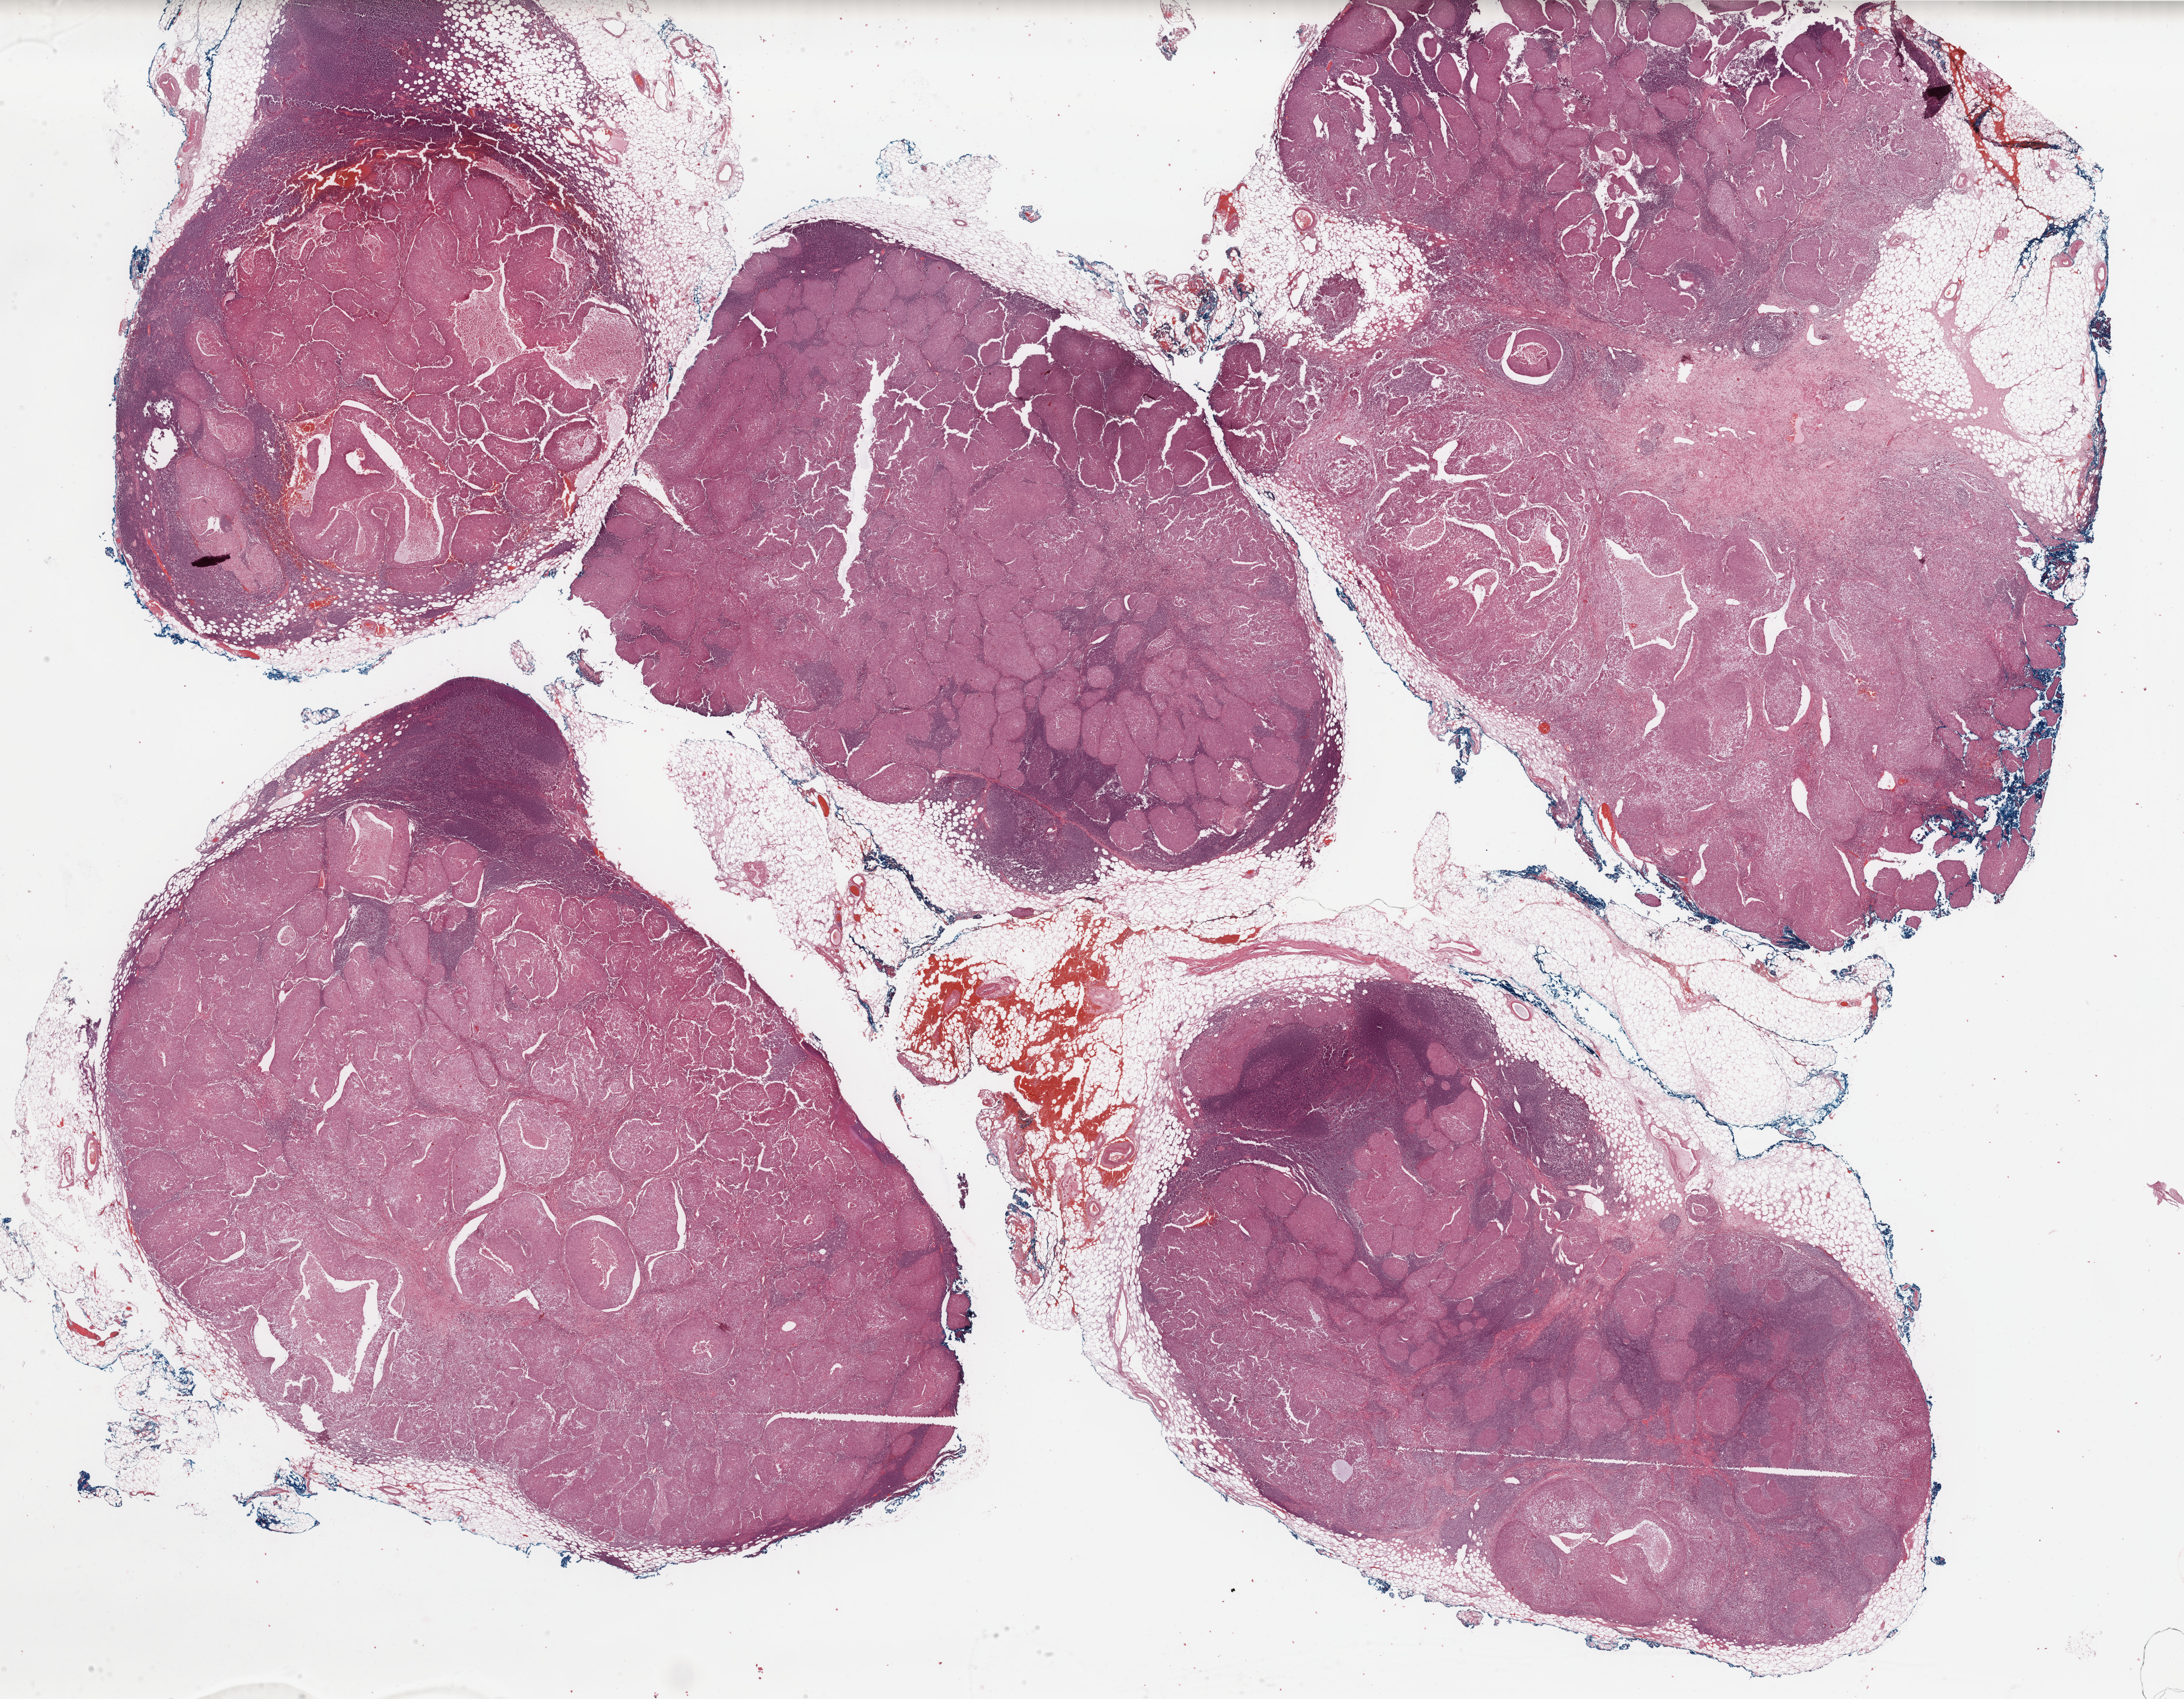
Hematoxylin and eosin (H&E) stained whole-slide image, whole scanned area (about 29.5 x 23.0 mm, acquisition: 40x scan) shown as a low-resolution overview; formalin-fixed paraffin-embedded (FFPE) diagnostic section; primary tumour sample from the cervix. Female, age 61 years at initial diagnosis. Histologic grade: G2 (moderately differentiated).
- FIGO stage: IIIB
- diagnosis: Squamous cell carcinoma, NOS (cervix uteri)